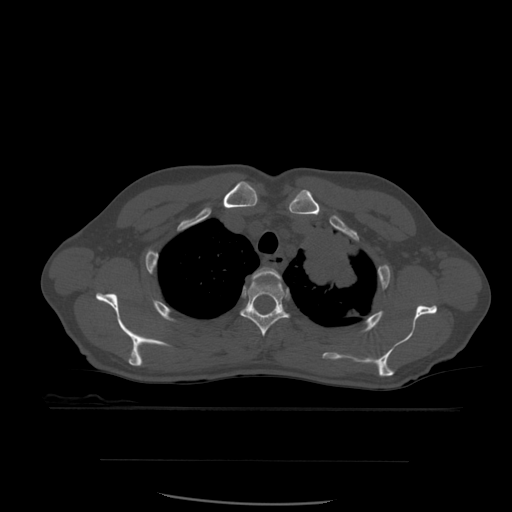
CT including the spine, one axial slice. Position 443 of 574 along the scan axis. Bone window (W 1800 / L 400 HU). 1.25 mm slice thickness. 512 × 512 image matrix. Patient age 48 years. Case-level facts recorded for this patient, not image findings: primary cancer: lung.
Structures marked on this image (semi-automatic segmentation, software-assisted and operator-edited):
- T2 vertebra: bounding box [x1, y1, x2, y2] px = [252, 268, 282, 282]
- T3 vertebra: [240, 279, 290, 337]